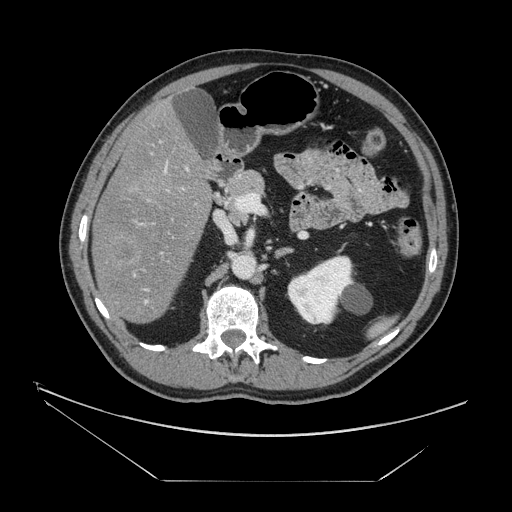
Contrast-enhanced abdominal CT, one axial slice. Slice 76 of 161 in the series (ordered by position). Reconstruction kernel STANDARD. 120 kVp. Soft-tissue window (W 400 / L 40 HU). 512 × 512 image matrix, field of view 440 × 440 mm. Male patient, age 65 years. From the clinical record (not read from this slice): diagnosis: colorectal cancer liver metastases, imaged before liver resection; multiple liver metastases: yes; largest metastasis: 4.2 cm; disease in both lobes: yes.
Outlined on this slice (manually delineated by an expert):
- hepatic veins: bounding box (x1, y1, x2, y2) in pixels: (134, 161, 168, 304)
- liver: (93, 105, 212, 323)
- planned liver remnant (the part of the liver to remain after resection): (187, 148, 198, 165)
- portal vein (with intrahepatic branches): (116, 167, 199, 312)
- liver metastasis: (126, 253, 131, 256)